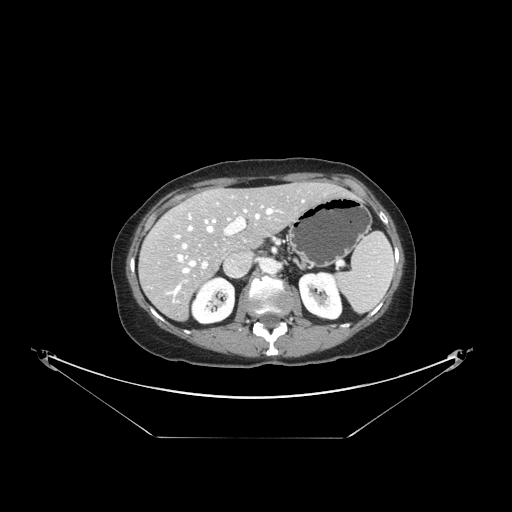
Contrast-enhanced abdominal CT, one axial slice. Slice 90 of 148 in the series (ordered by position). Reconstruction kernel STANDARD. Intravenous contrast given. Soft-tissue window (W 400 / L 40 HU). 2.5 mm slice thickness. 512 × 512 image matrix. Female patient, age 73 years. Case-level facts recorded for this patient, not image findings: diagnosis: colorectal cancer liver metastases, imaged before liver resection; multiple liver metastases: no; largest metastasis: 1 cm.
Structures marked on this image (manually delineated by an expert):
- hepatic veins: bounding box [x1, y1, x2, y2] px = [172, 208, 274, 295]
- liver: [141, 184, 347, 319]
- planned liver remnant (the part of the liver to remain after resection): [168, 183, 347, 254]
- portal vein (with intrahepatic branches): [174, 206, 263, 269]